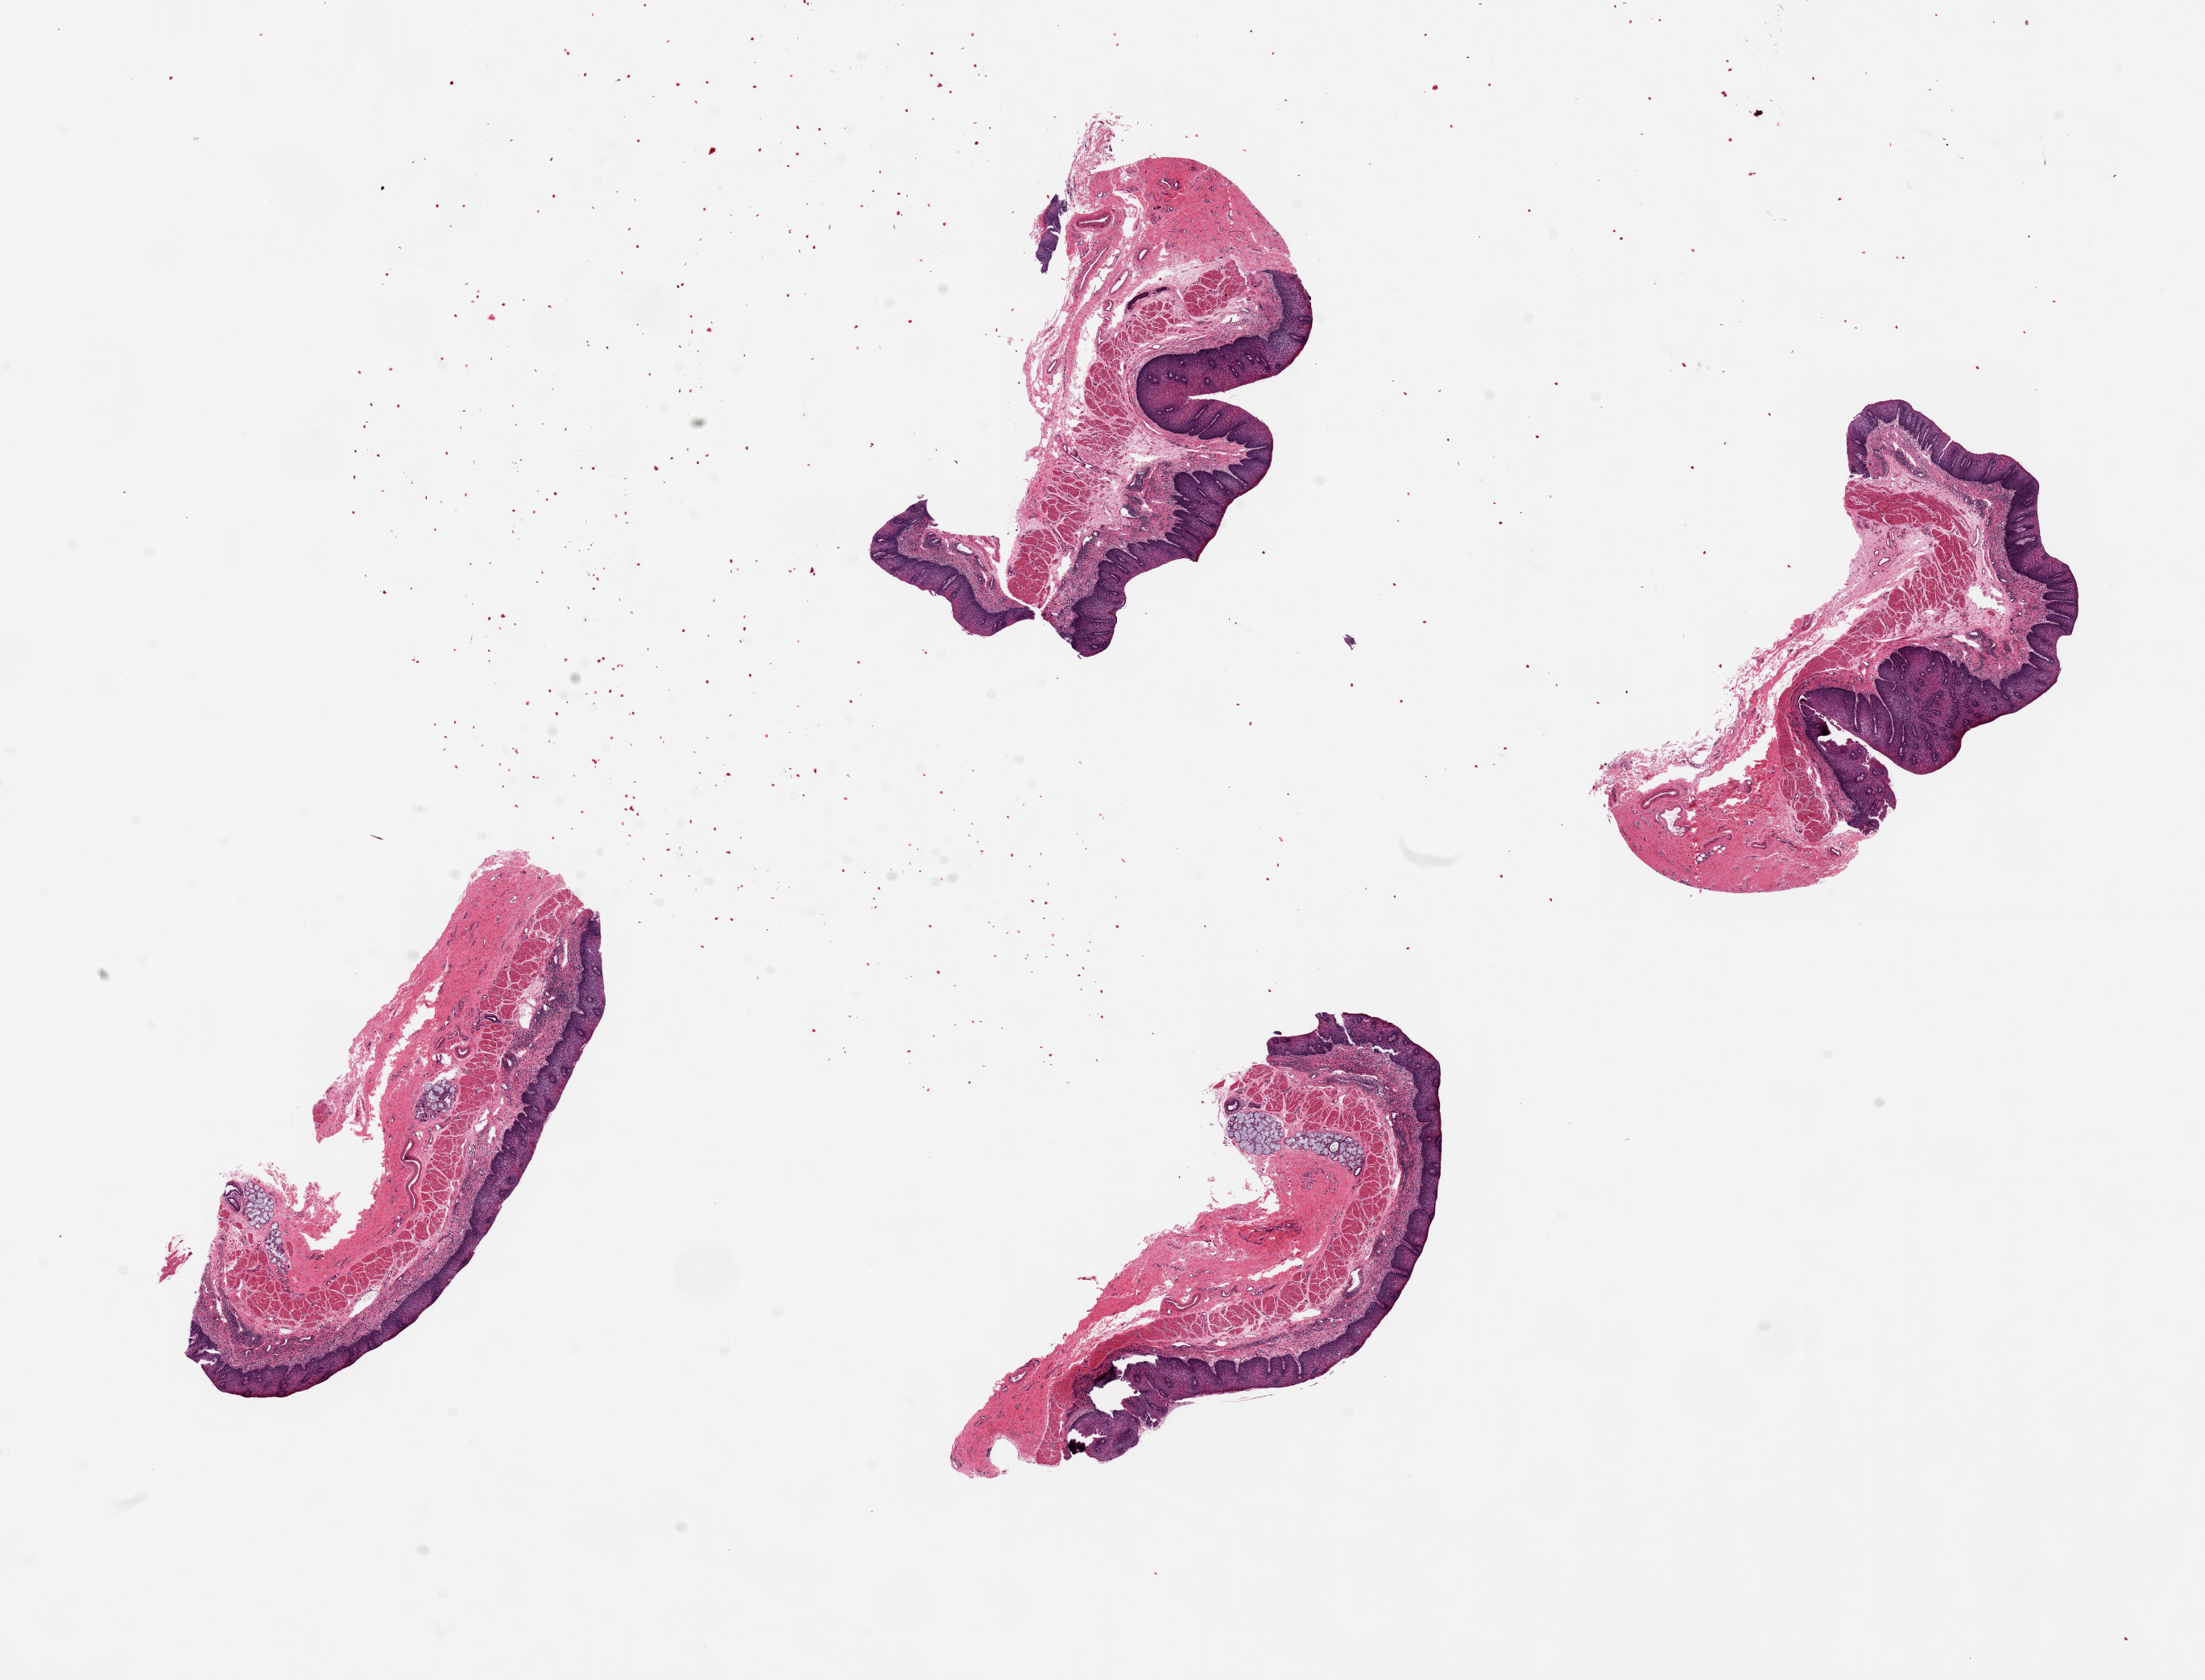
Haematoxylin and eosin whole-slide image — whole scanned area (about 21.7 x 16.5 mm) shown as a low-resolution overview; PAXgene-fixed, paraffin-embedded tissue; section of esophageal mucous membrane (target tissue); donor tissue sample.
Review note (as recorded): 6 pieces ~5x2mm, squamous mucosa is ~20% of thickness. should be labeled mucosa.